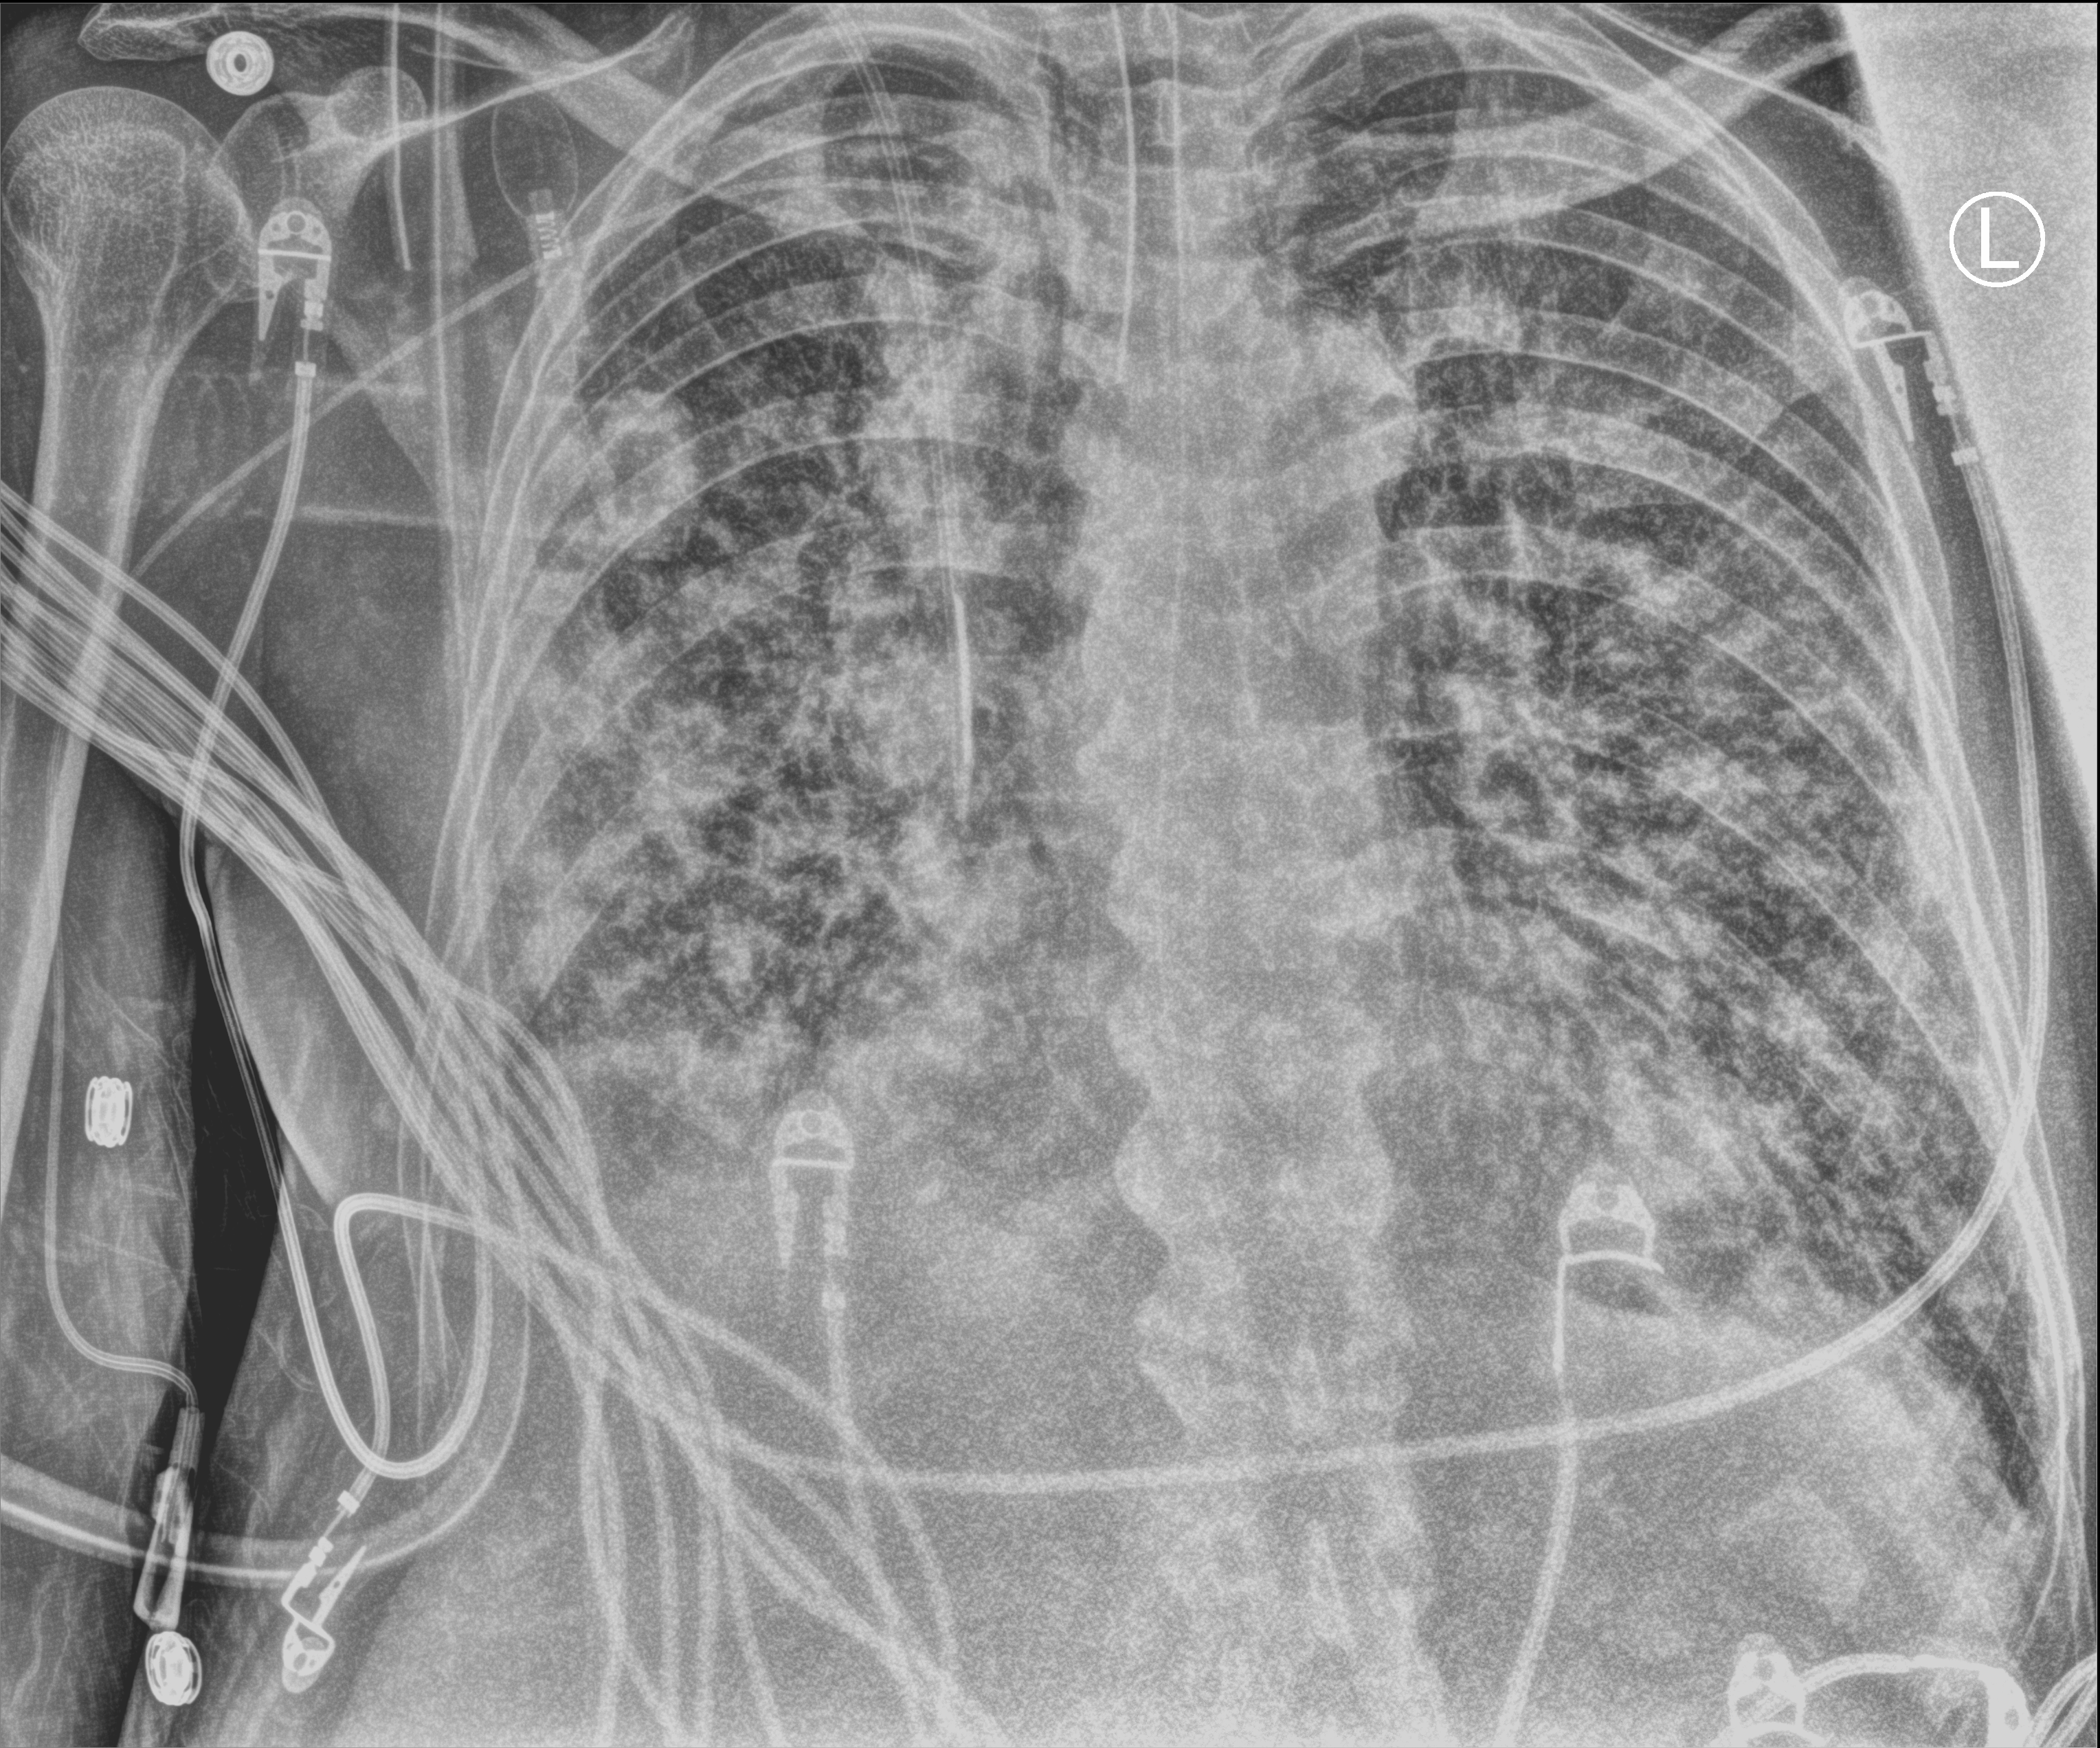
Chest X-ray (portable); anteroposterior (AP) projection. Male patient hospitalised with COVID-19, age 60–74 years.
Admission-level facts for this patient (not findings on this image; timing relative to this image not recorded): admitted to intensive care during this hospital stay: yes; other chronic lung disease (admission record): no.